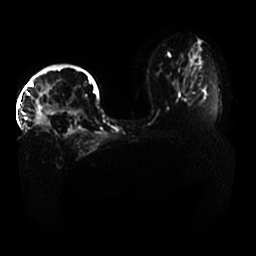
Breast MRI, one axial slice; slice 22 of 33 in the series (ordered by position); diffusion-weighted series; image 2 of 4 stored at this slice position (different b-values; order by instance number); 1.5 T; 256 × 256 image matrix, field of view 400 × 400 mm. Female patient.
Annotated regions visible in this slice (outlined manually by an expert reader):
- tumour on diffusion-weighted imaging: box from (x=32, y=100) to (x=51, y=132) px